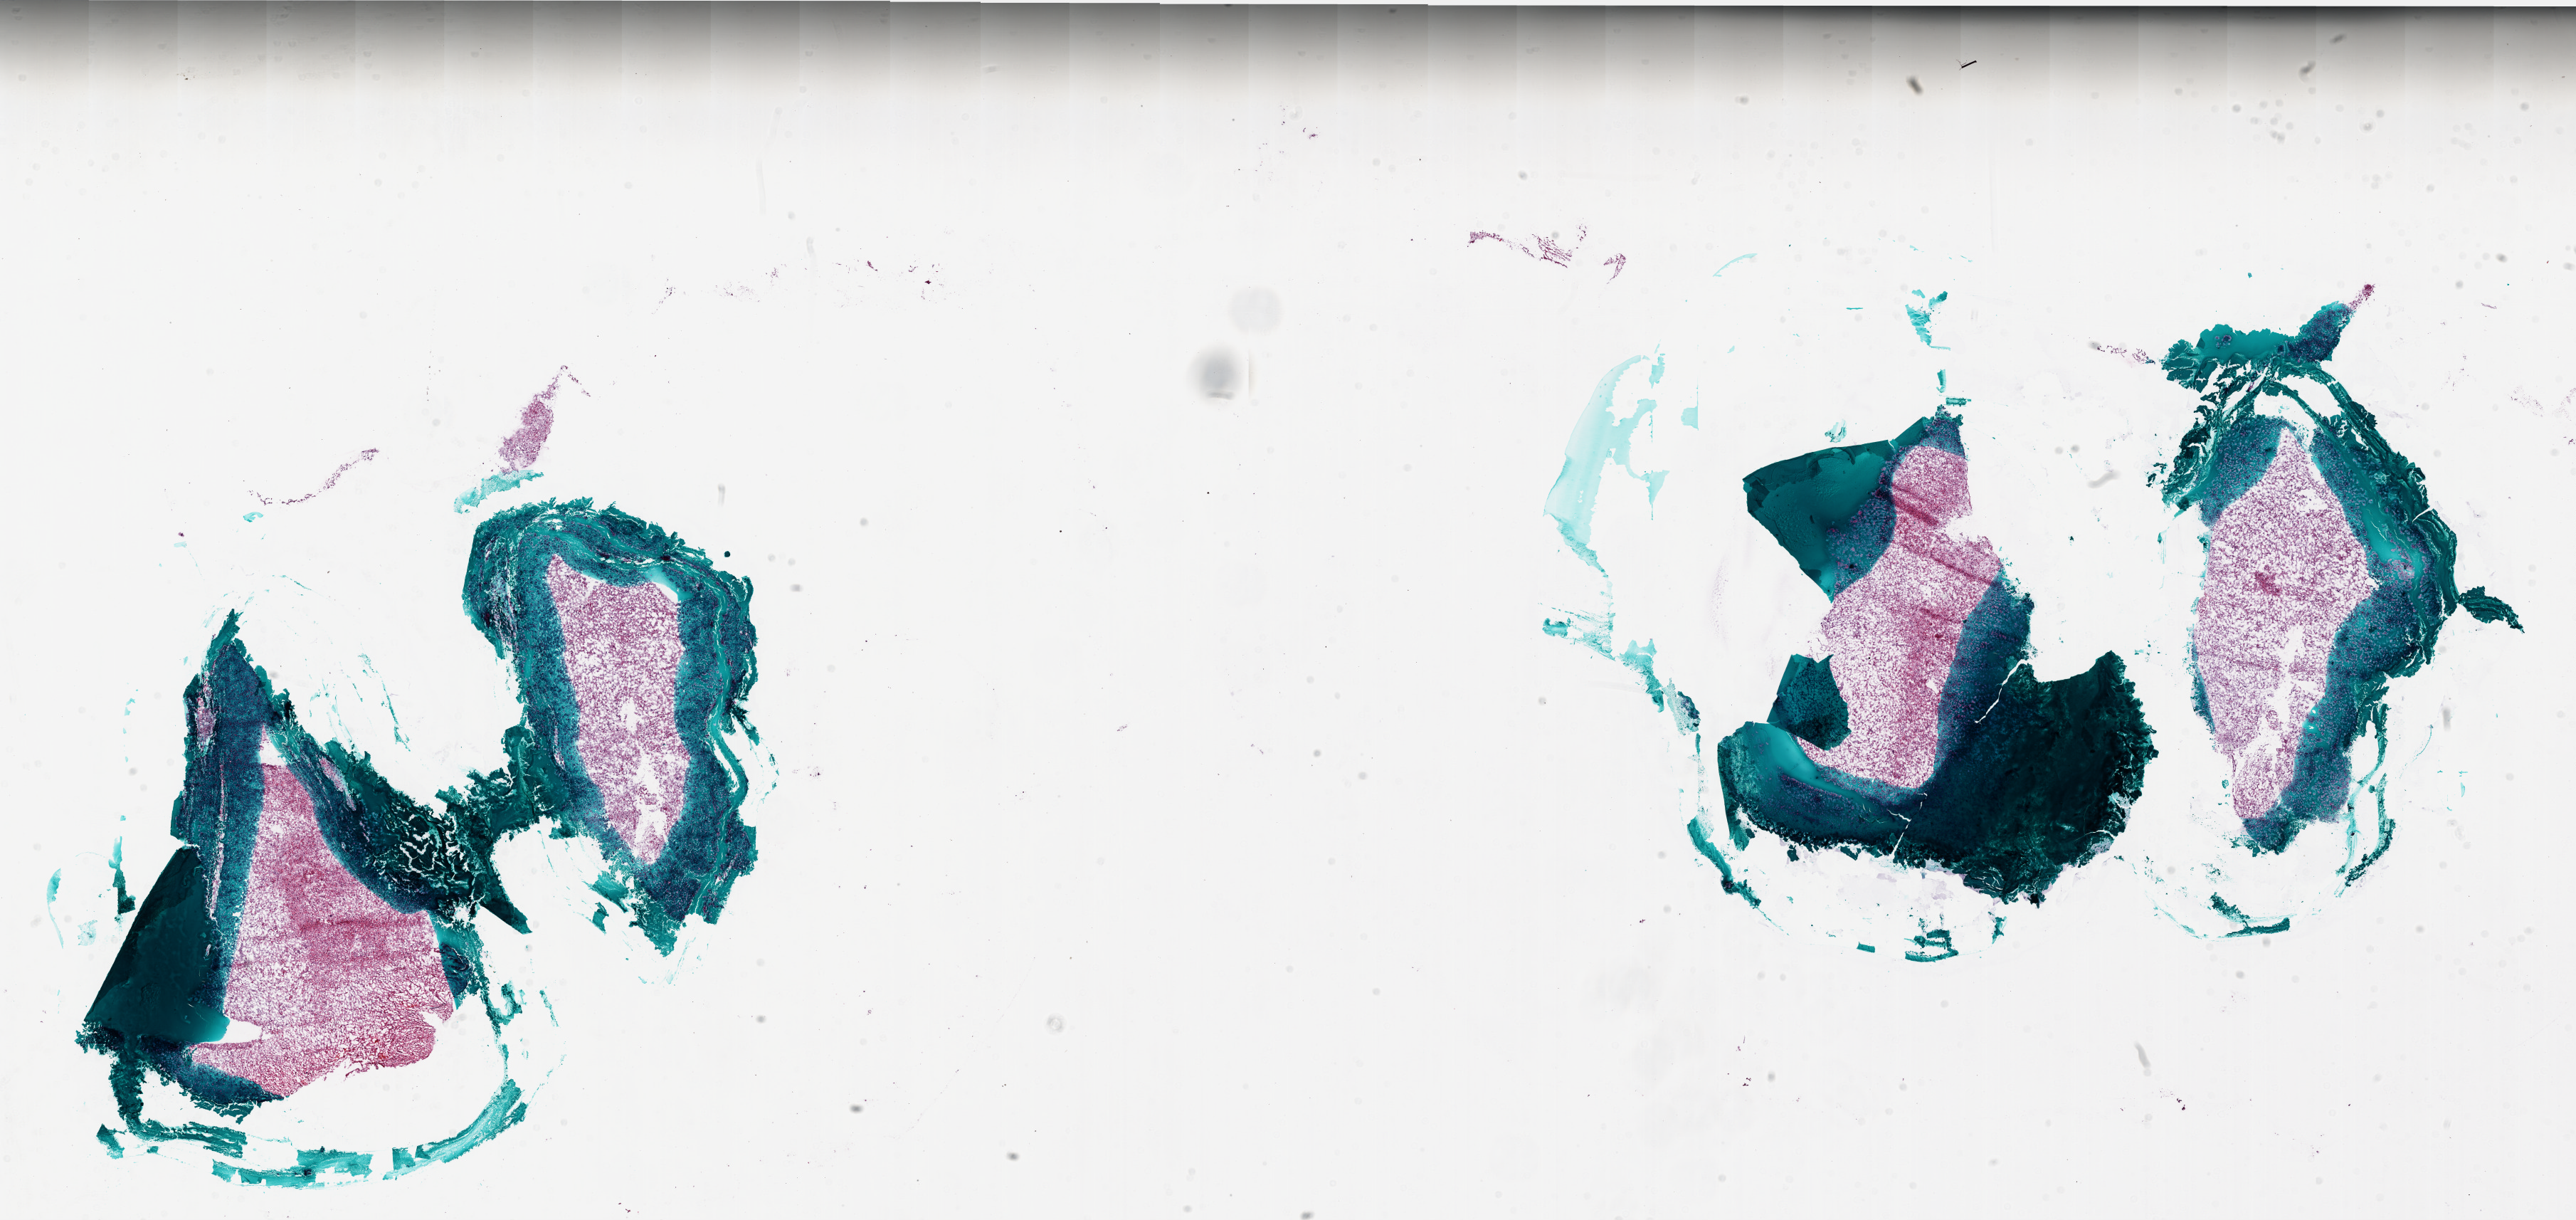
H&E whole-slide image — a low-resolution overview of the entire scanned area, about 29.0 x 13.7 mm (slide scanned at 20x); frozen section from the bottom of the tissue portion; brain, primary tumour sample. Female, age 36 years at initial diagnosis. Composition of this section per pathologist review: tumour cells 100%, tumour nuclei 100%.
Histologic diagnosis: Glioblastoma.